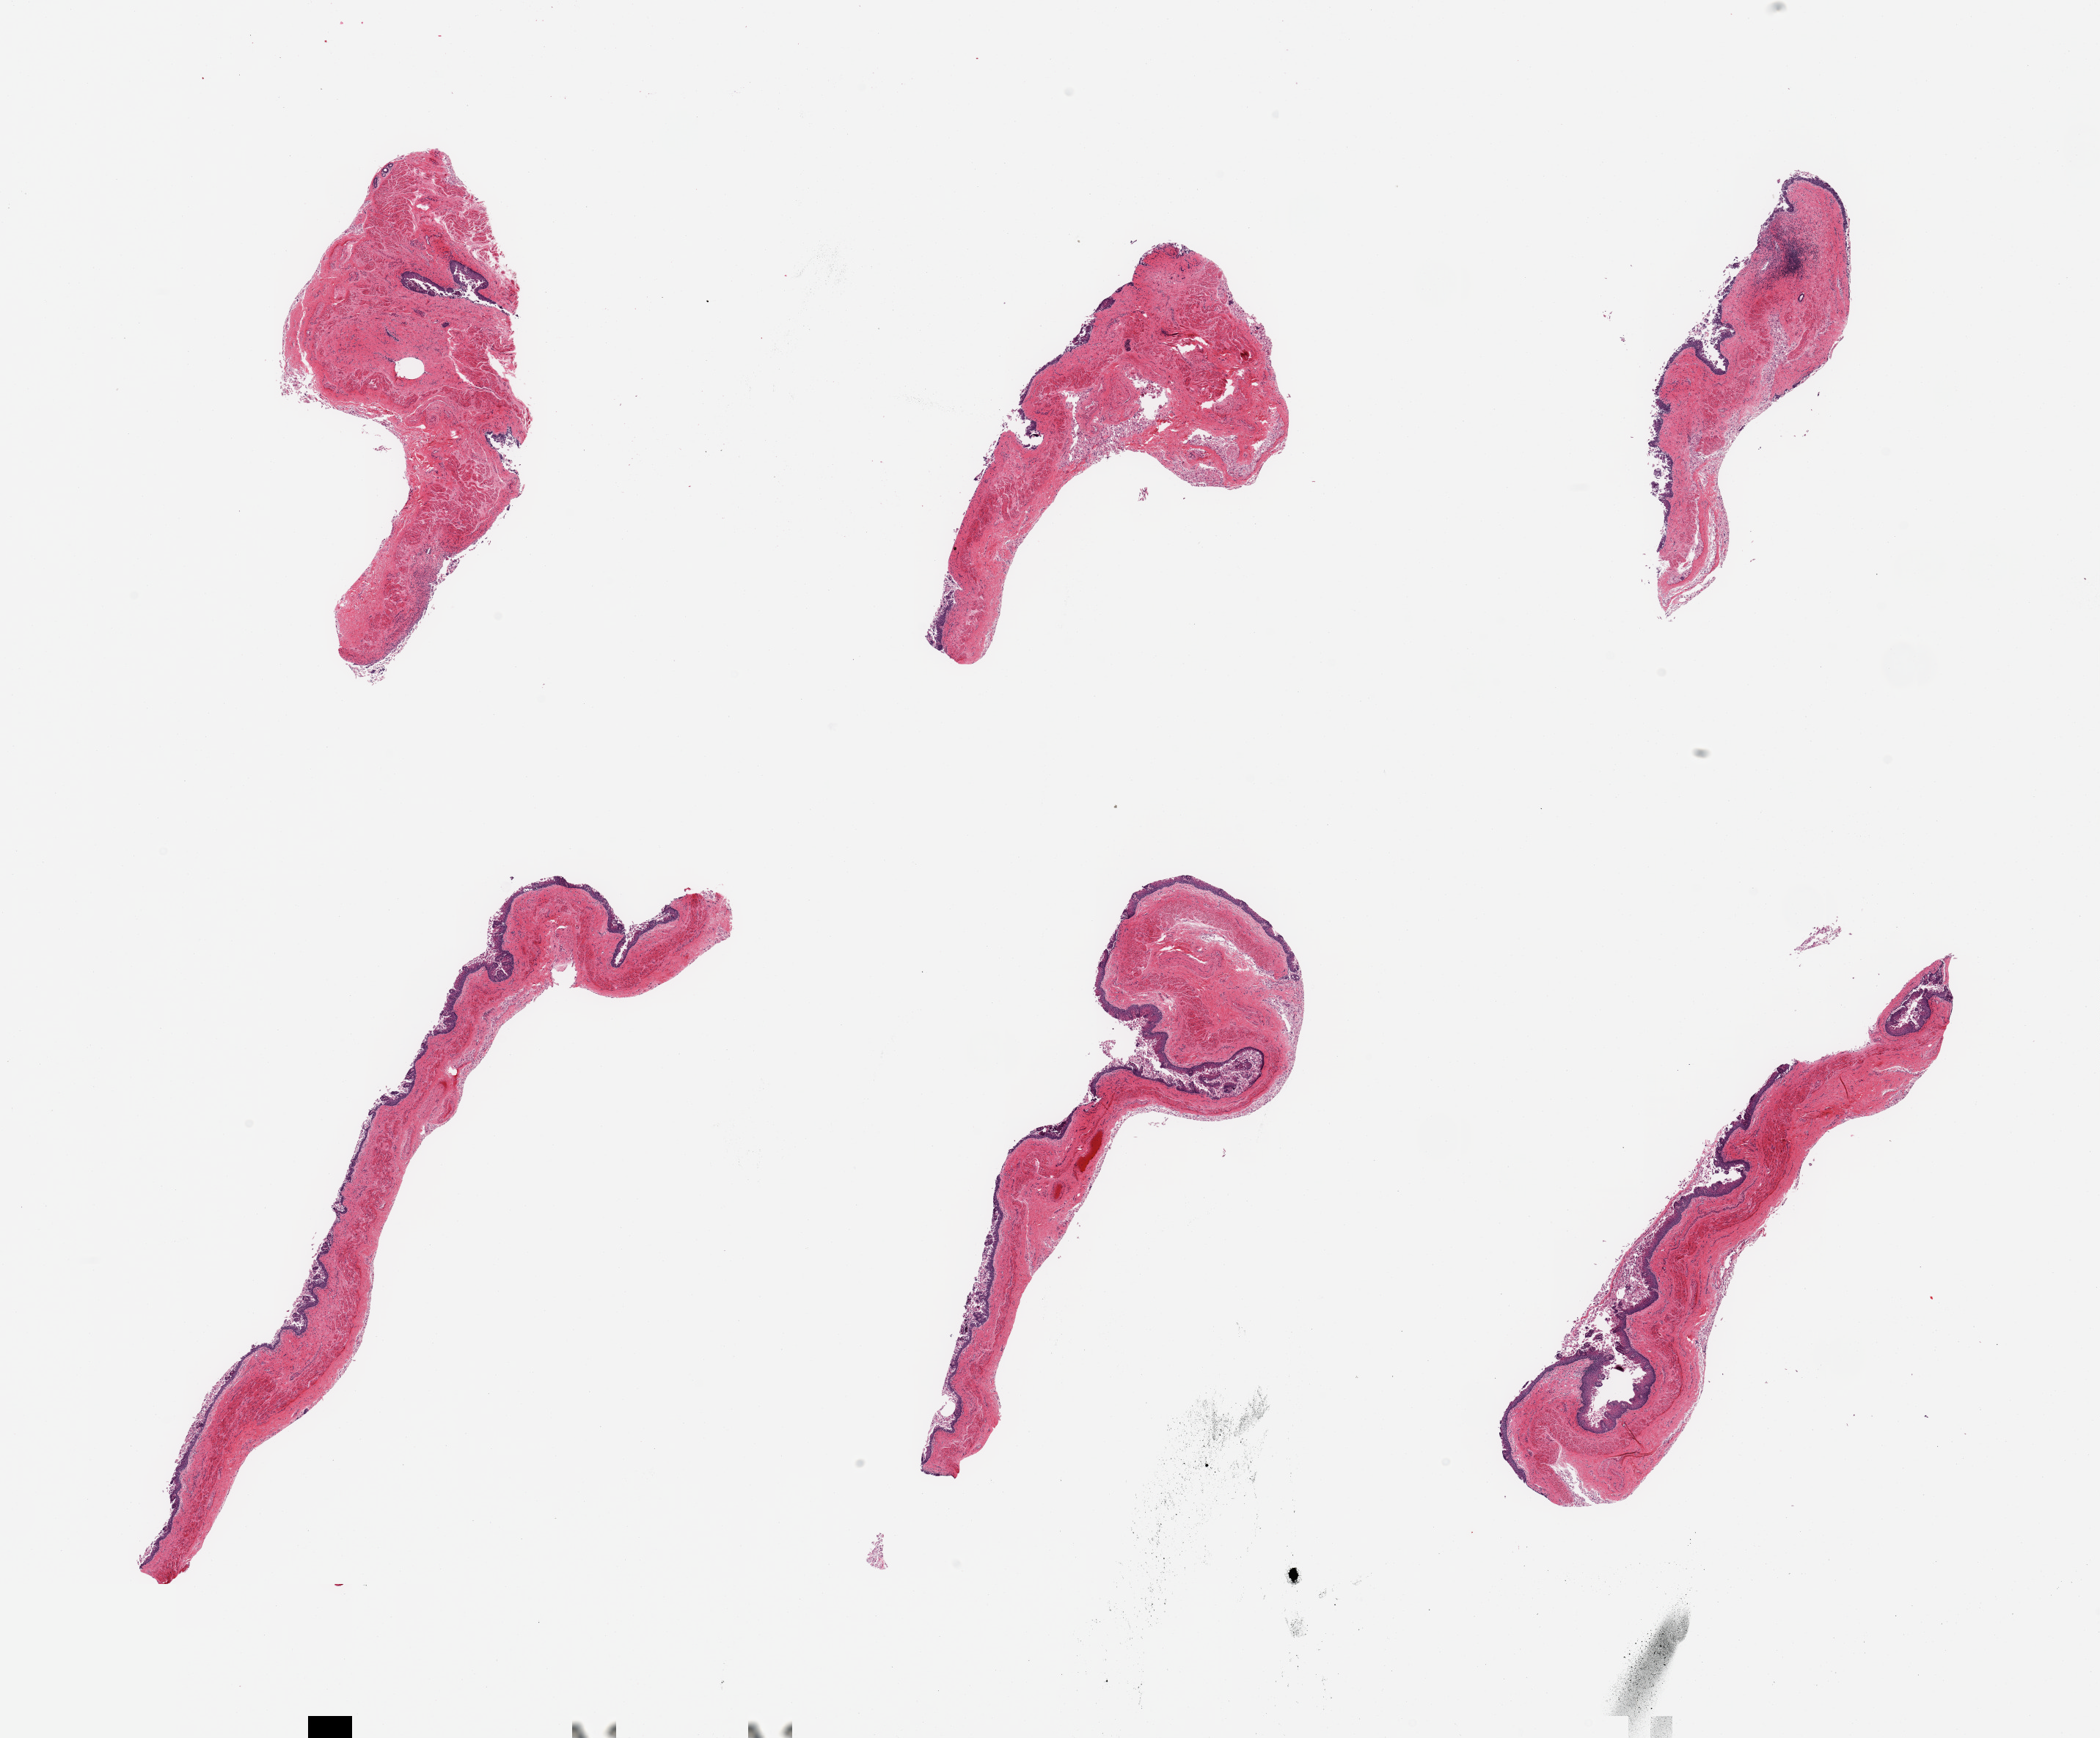
H&E whole-slide image, brightfield — shown as a low-resolution overview of the whole scanned area (about 22.6 x 18.7 mm), PAXgene-fixed paraffin-embedded (PFPE) section, sampled site (target tissue): esophageal mucous membrane, donor tissue sample. Donor: female.
* pathologist's review note for this sample: 6 pieces; epithelium largely sloughed